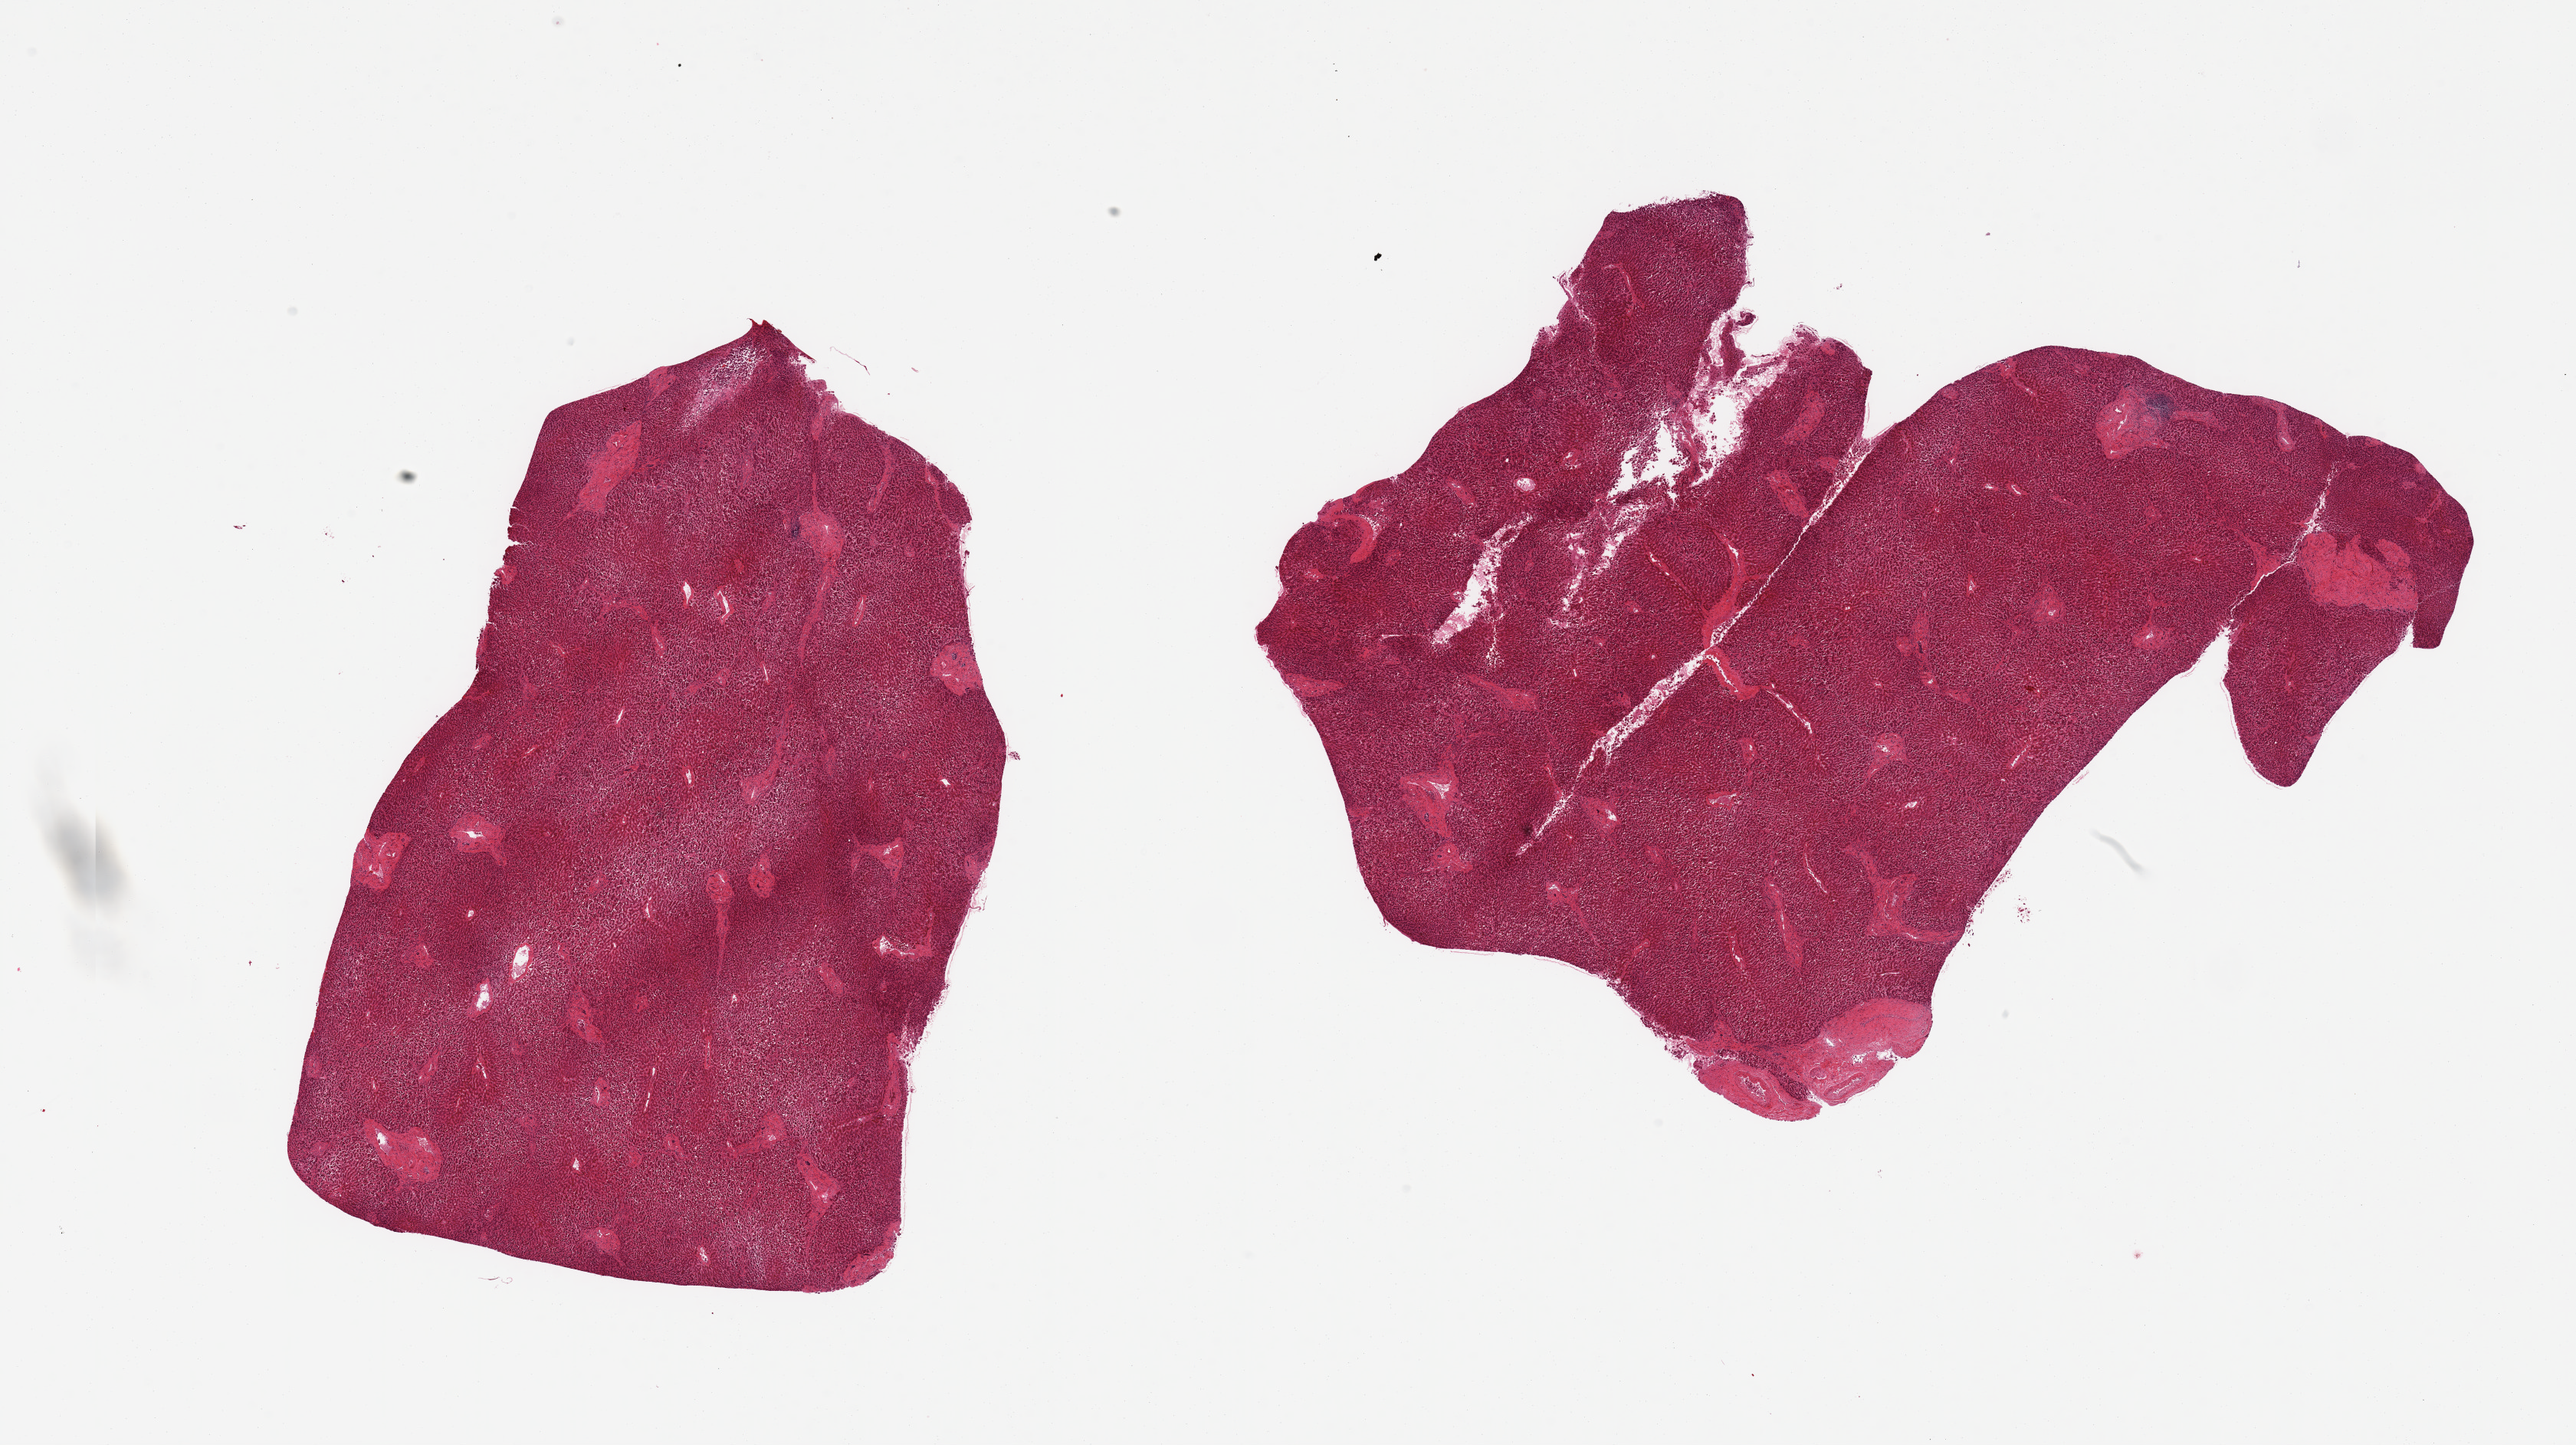
Whole-slide image, hematoxylin and eosin (H&E) stain, brightfield — whole scanned area (about 26.6 x 14.9 mm, from a 20x scan) shown as a low-resolution overview, PAXgene-fixed, paraffin-embedded tissue, target tissue: liver, tissue donor sample.
Pathologist's review note for this sample: 2 pieces; periportal fragmentation of cord cells greater than central.